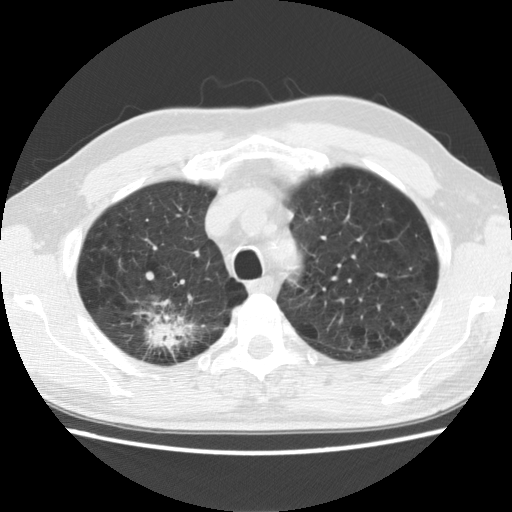
Low-dose screening chest CT, one axial slice. Position 108 of 142 along the scan axis. 120 kVp. Lung window (W 1500 / L -600 HU). 2.5 mm slice thickness. 512 × 512 image matrix, field of view 340 × 340 mm.
Structures marked on this image (outlined manually by an expert reader):
- lesion 1 (tumor, upper lobe of right lung): box from (x=148, y=322) to (x=175, y=348) px